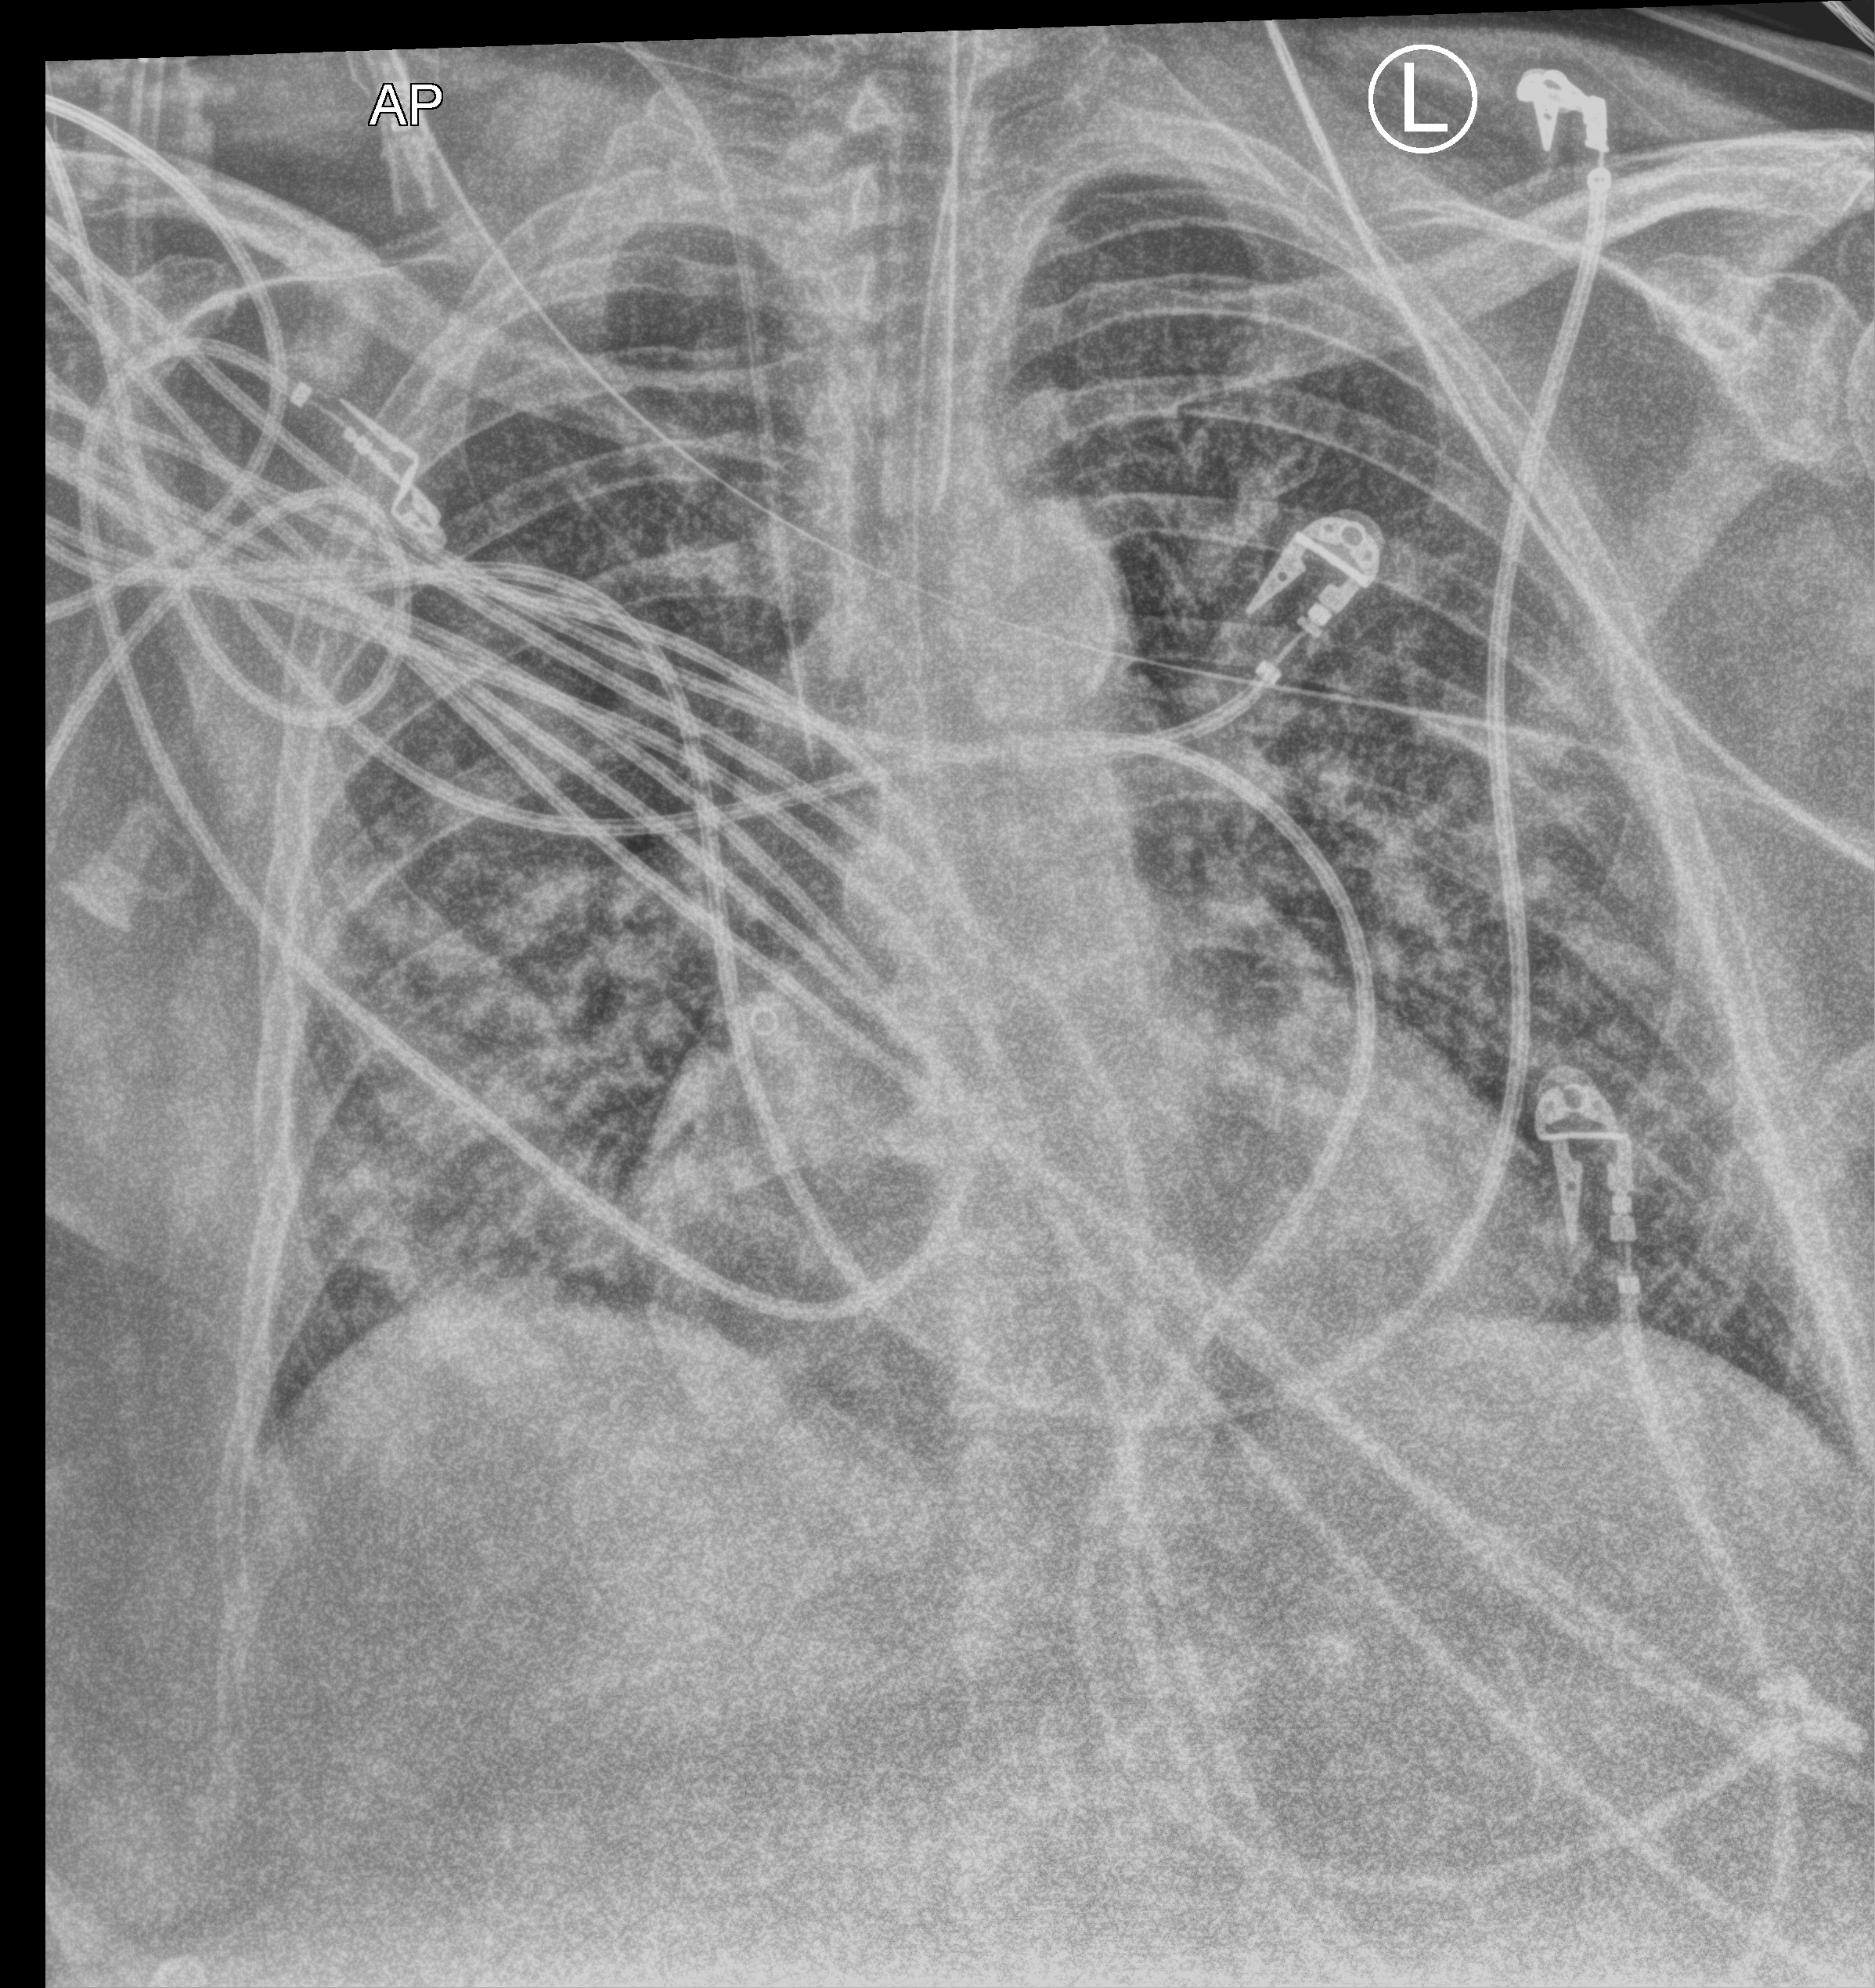
Chest X-ray (portable), anteroposterior (AP) projection. Patient hospitalised with COVID-19; female, aged 75–90 years.
Admission-level facts for this patient (not findings on this image; timing relative to this image not recorded):
- diabetes (admission record): no
- admitted to intensive care during this hospital stay: yes